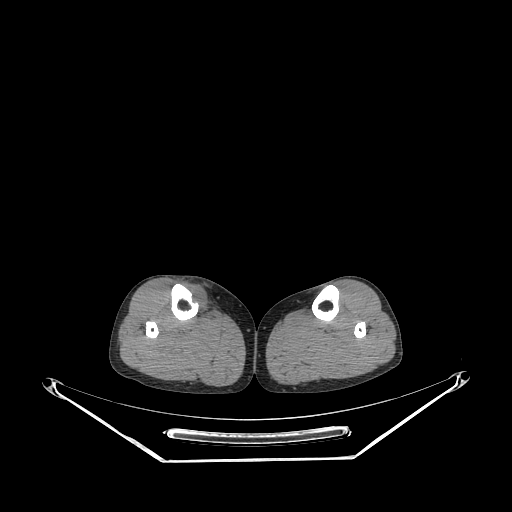
CT of an extremity soft-tissue mass (from a PET/CT study), one axial slice; slice 137 of 267 in the series (ordered by position); soft-tissue window (W 400 / L 40 HU); 3.75 mm slice thickness; 512 × 512 image matrix, field of view 500 × 500 mm. Female patient. From the clinical record (not read from this slice): histological type: undifferentiated – high grade; grade: high; site of the primary tumour: right thigh.
Annotated regions visible in this slice (expert contour drawn on MRI and transferred to this co-registered scan by the dataset authors):
- gross tumour volume (mass): bounding box [x1, y1, x2, y2] px = [185, 285, 209, 314]